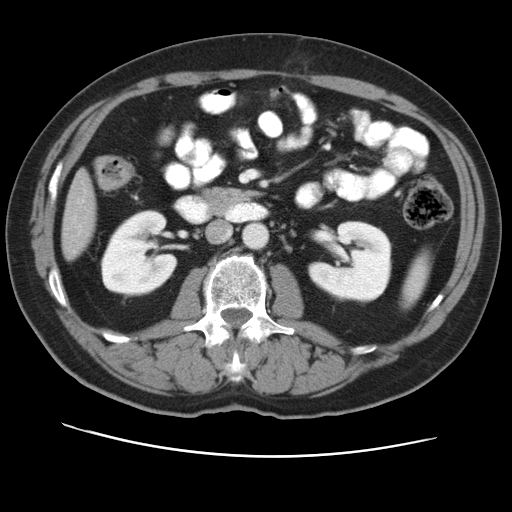
Contrast-enhanced abdominal CT, one axial slice. 120 kVp. Intravenous contrast given. Soft-tissue window (W 400 / L 40 HU). 5 mm slice thickness. 512 × 512 image matrix. Male patient, age 59 years. Case-level facts recorded for this patient, not image findings: diagnosis: colorectal cancer liver metastases, imaged before liver resection; multiple liver metastases: yes; largest metastasis: 6.3 cm; disease in both lobes: yes.
Annotated regions visible in this slice (expert manual segmentation):
- liver: bounding box (x1, y1, x2, y2) in pixels: (62, 174, 96, 257)
- planned liver remnant (the part of the liver to remain after resection): (68, 174, 96, 216)